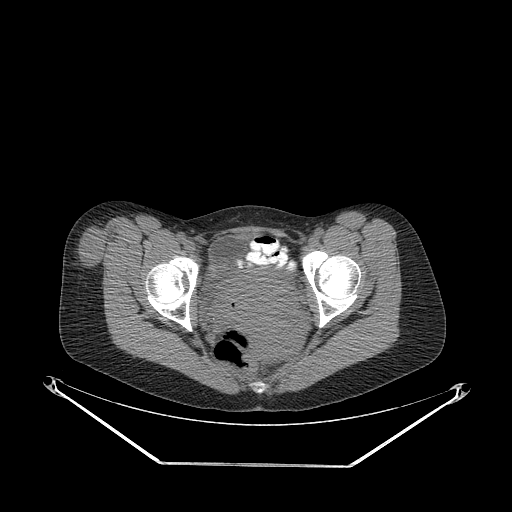
CT of an extremity soft-tissue mass (from a PET/CT study), one axial slice. Slice 69 of 267 in the series (ordered by position). Reconstruction kernel STANDARD. 140 kVp. Soft-tissue window (W 400 / L 40 HU). 3.75 mm slice thickness. 512 × 512 image matrix, field of view 500 × 500 mm. Female patient. Case-level facts recorded for this patient, not image findings: histological type: synovial sarcoma; grade: intermediate; site of the primary tumour: right thigh.
Outlined on this slice (expert contour drawn on MRI and transferred to this co-registered scan by the dataset authors):
- gross tumour volume including surrounding oedema: bounding box [x1, y1, x2, y2] px = [77, 226, 113, 270]
- gross tumour volume (mass): [77, 228, 111, 270]